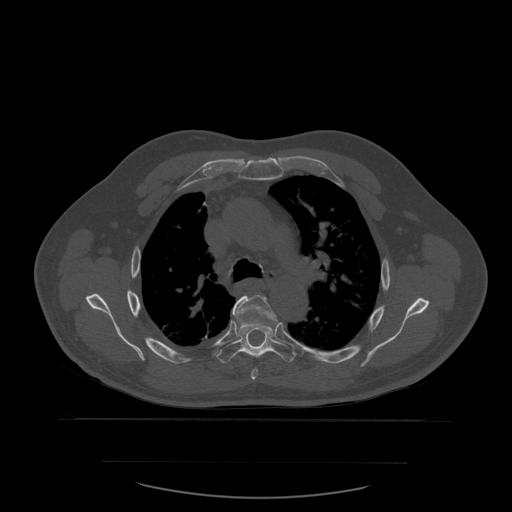
CT including the spine, one axial slice. Position 412 of 590 along the scan axis. Bone window (W 1800 / L 400 HU). 1.25 mm slice thickness. 512 × 512 image matrix, field of view 479 × 479 mm. Patient age 71 years. From the clinical record (not read from this slice): primary cancer: lung.
Annotated regions visible in this slice (semi-automatically segmented with operator editing):
- T5 vertebra: bounding box <234,295,277,380> (left, top, right, bottom; pixels)
- T6 vertebra: <217,307,296,364>